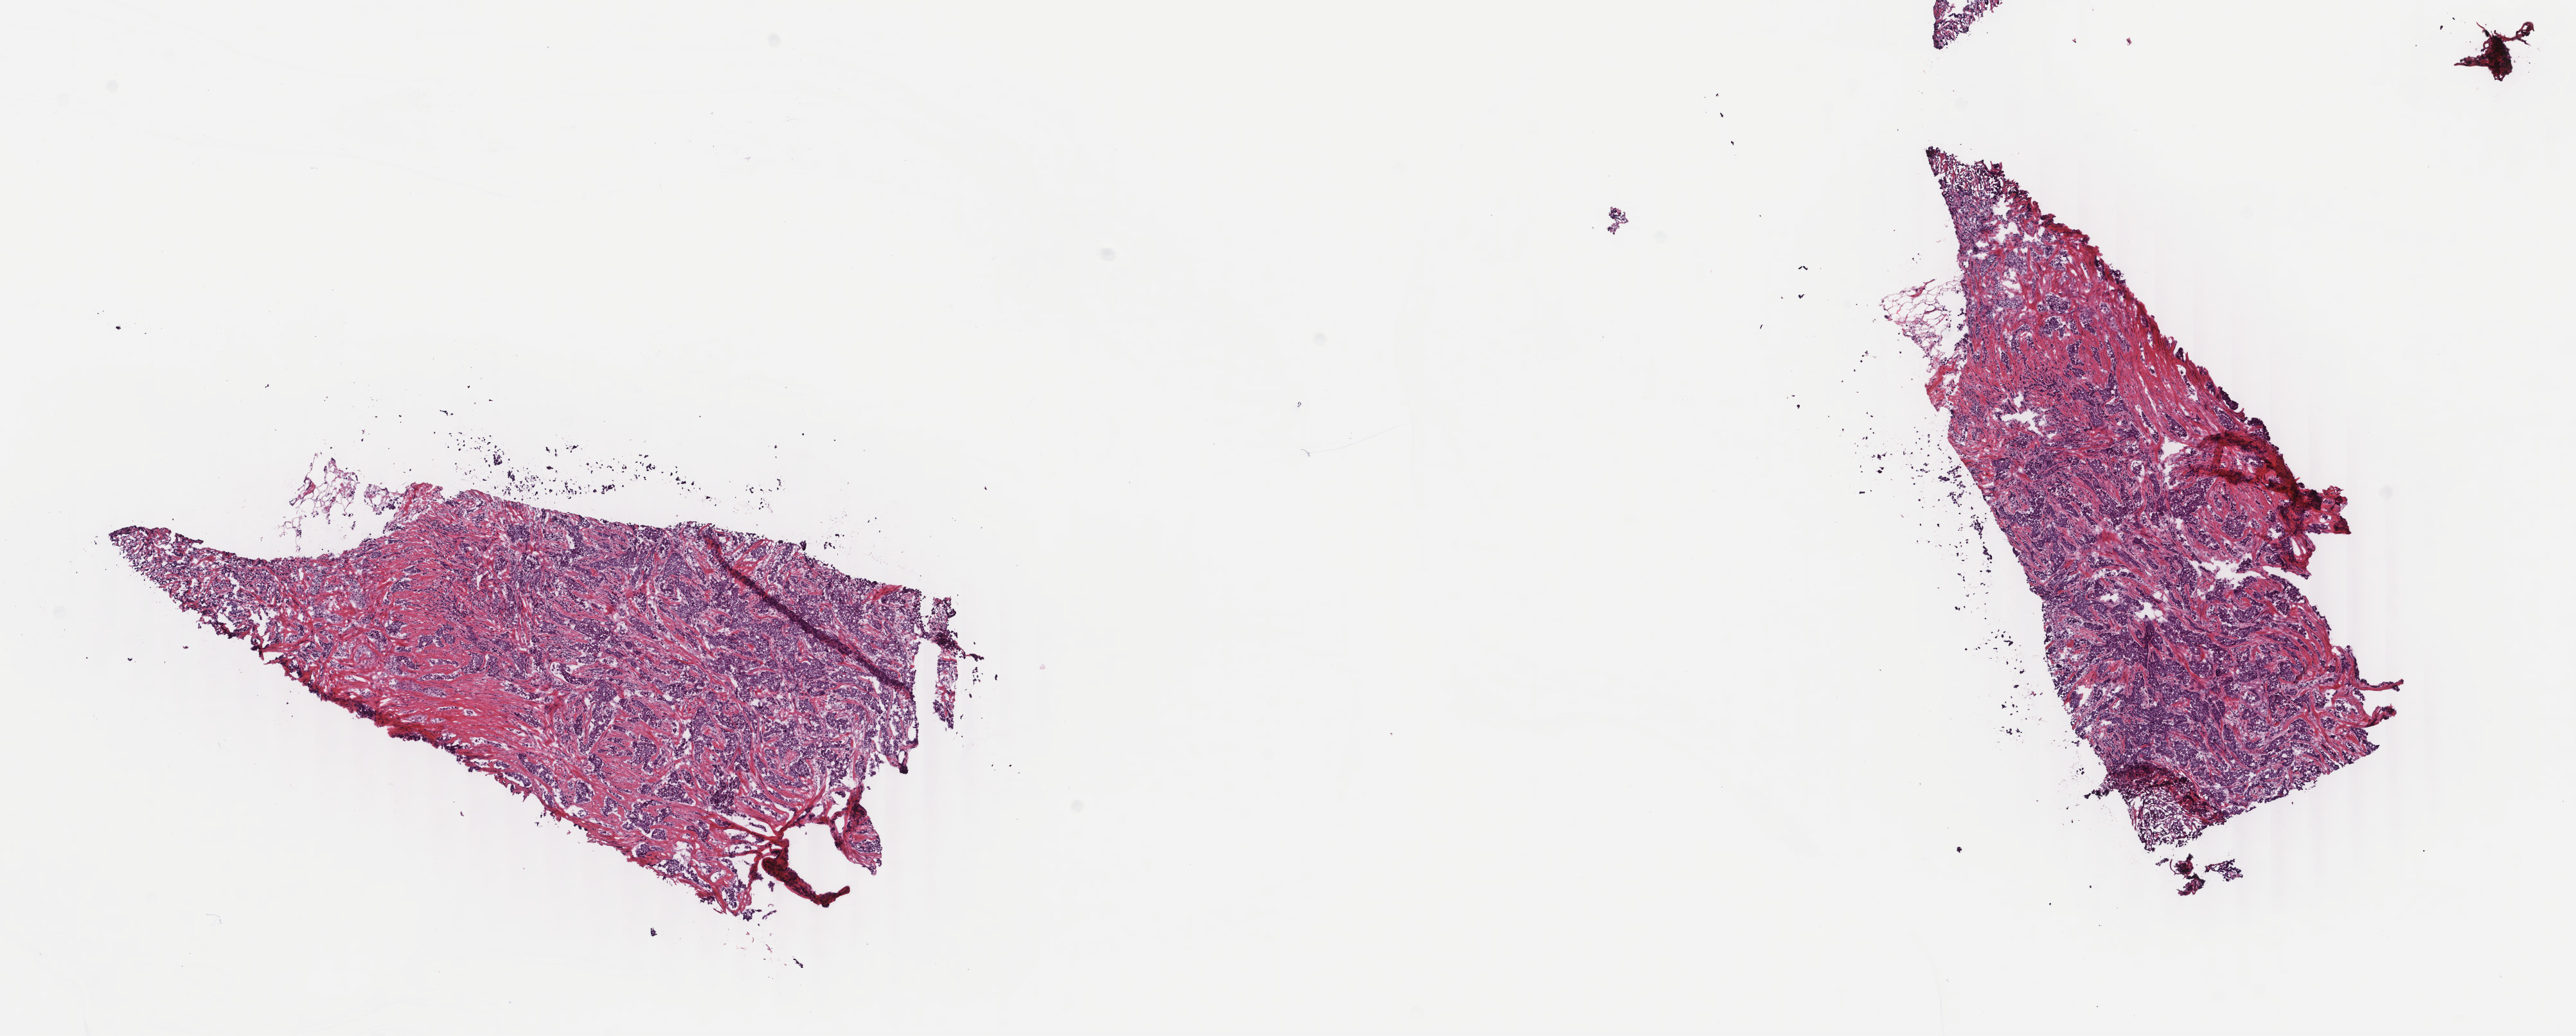
Whole-slide histology image, H&E, a low-resolution overview of the entire scanned area, about 15.9 x 6.4 mm (slide scanned at 40x); frozen section from the top of the tissue portion; breast, primary tumour sample. Patient: female, age at initial diagnosis 54 years. Pathologist review of this section (percent, as recorded): tumour cells 85%, tumour nuclei 85%, normal cells 0%, stromal cells 14%, necrosis 1%. Infiltration values recorded for this section: lymphocyte infiltration 2%, monocyte infiltration 1%, neutrophil infiltration 1%.
Diagnosis: Infiltrating duct carcinoma, NOS. Lymph nodes positive (case pathology): 0 of 4 examined. AJCC pathologic stage: I (6th edition).